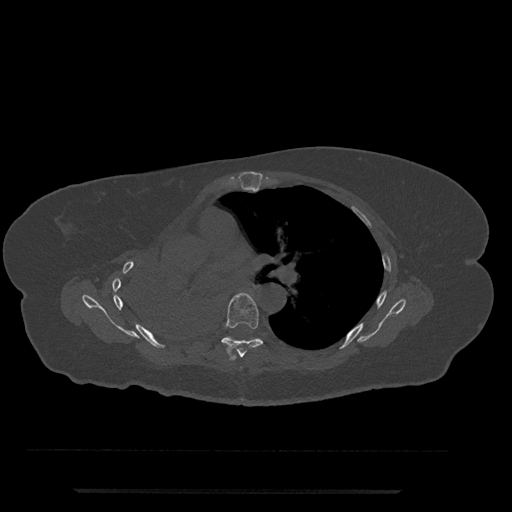
CT including the spine, one axial slice. Position 491 of 797 along the scan axis. Reconstruction kernel Br40s/3. 120 kVp. Bone window (W 1800 / L 400 HU). 0.5 mm slice thickness. 512 × 512 image matrix, field of view 440 × 440 mm. Patient: female, 51 years. From the clinical record (not read from this slice): primary cancer: neuro; vertebrae with lytic lesions (as recorded): T8.
Annotated regions visible in this slice (semi-automatically segmented with operator editing):
- T6 vertebra: box from (x=221, y=293) to (x=263, y=359) px
- T7 vertebra: (x=227, y=337)–(x=253, y=340)